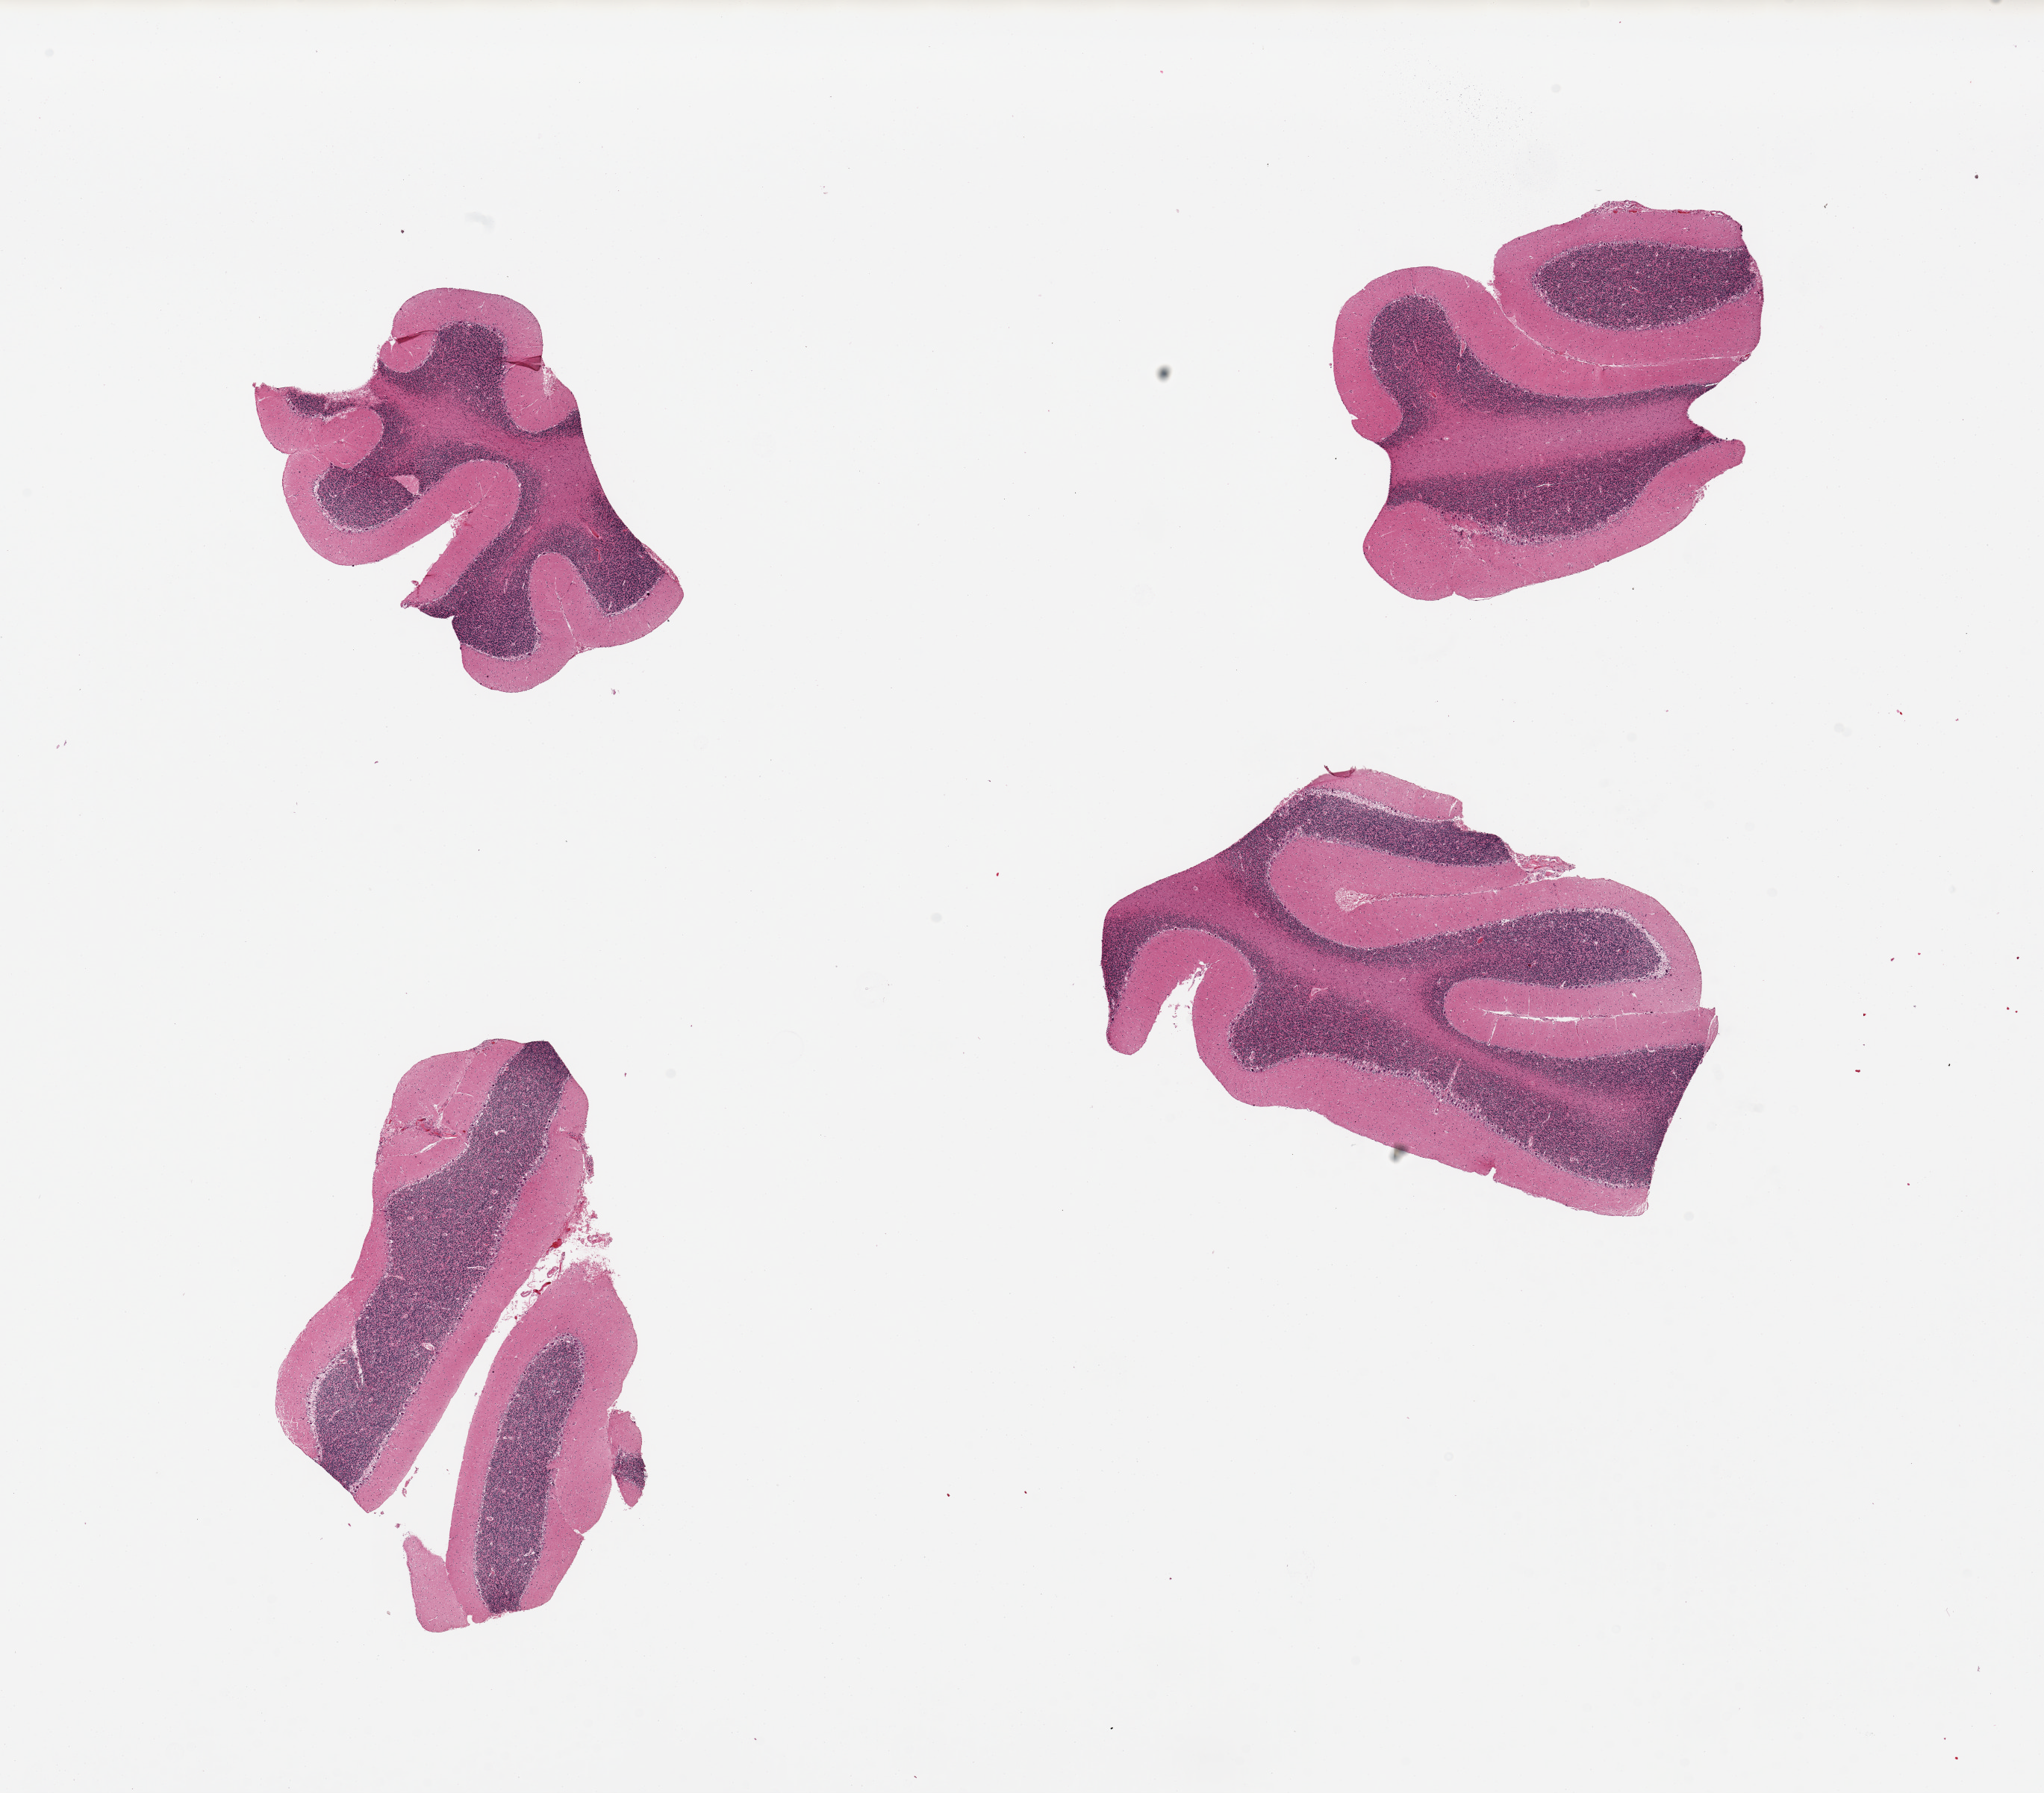
Haematoxylin and eosin whole-slide image, shown as a low-resolution overview of the whole scanned area (about 21.7 x 19.0 mm), PAXgene-fixed paraffin-embedded (PFPE) section, target tissue: cerebellum, tissue donor sample.
Review note (as recorded): 4 pieces, Purkinje cells show minimal ischemic damage.